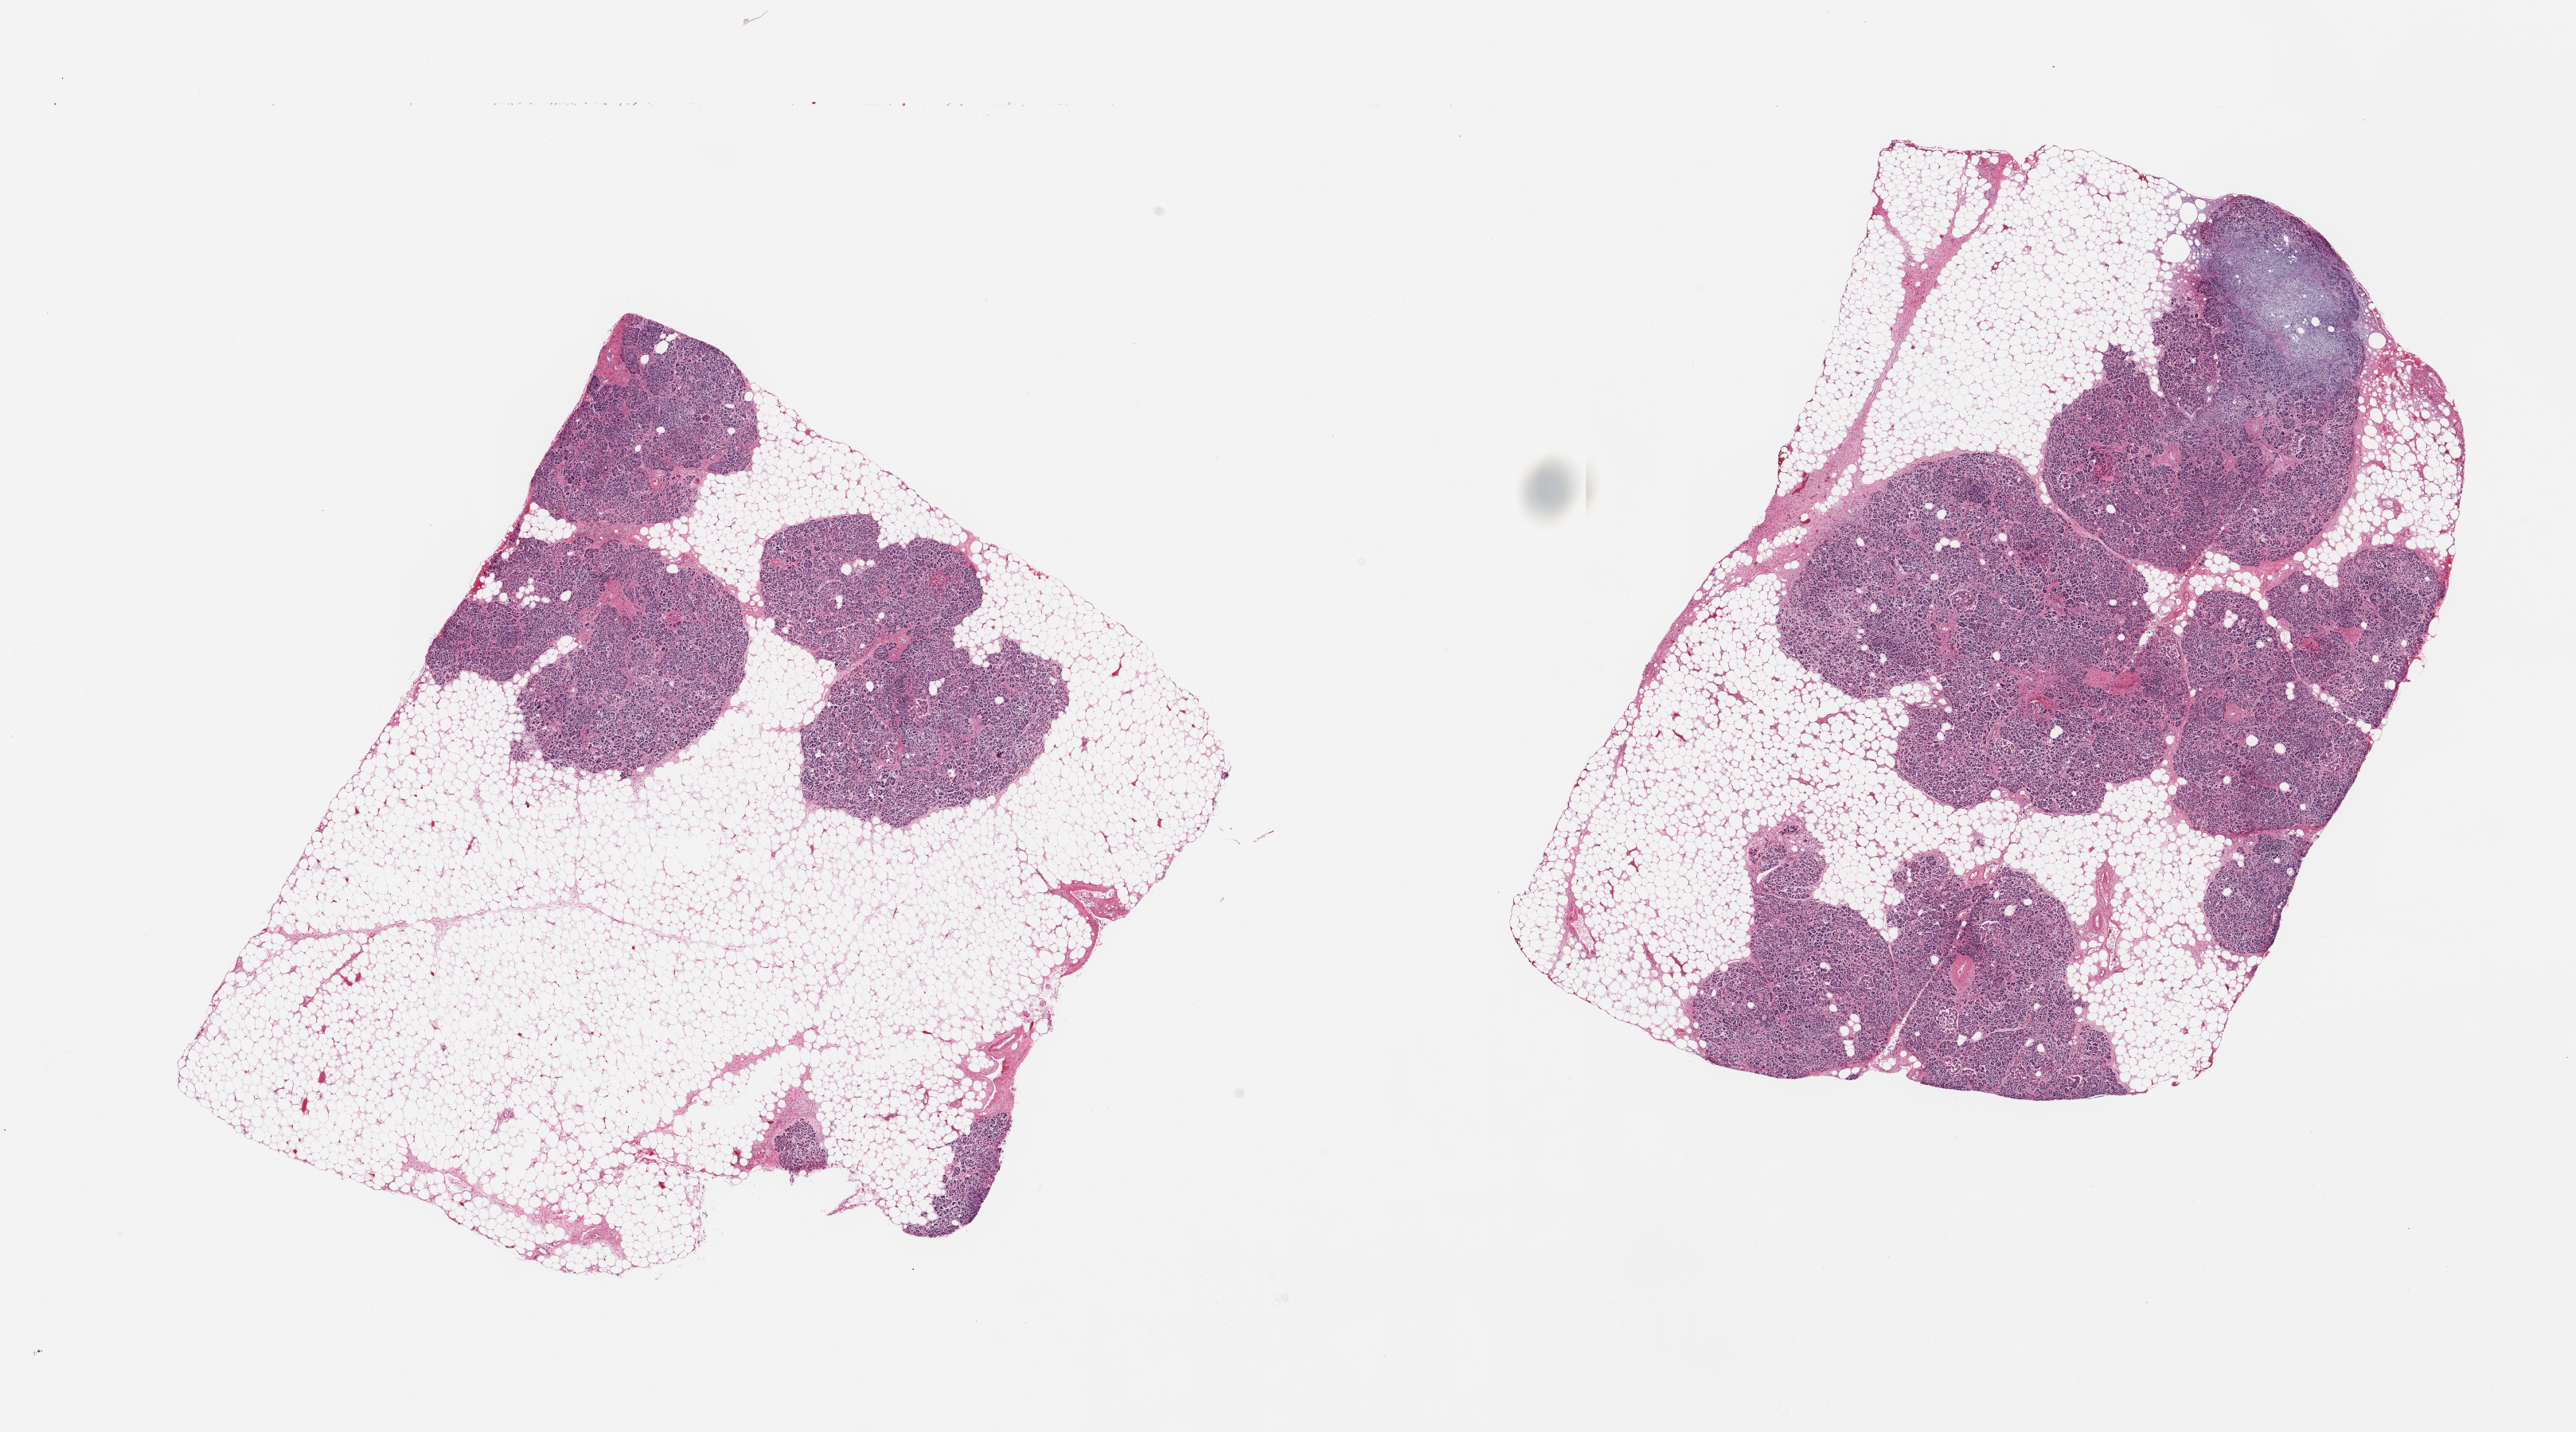
Digitized hematoxylin and eosin (H&E)-stained section, low-resolution overview of the scanned area, about 25.6 x 14.2 mm (from a 20x scan); PAXgene-fixed, paraffin-embedded tissue; section of pancreas (target tissue); donor tissue sample.
Pathologist's review note for this sample: 2 pieces; 50% fat content; focal severe autolysis; slight interstitial fibrosis.